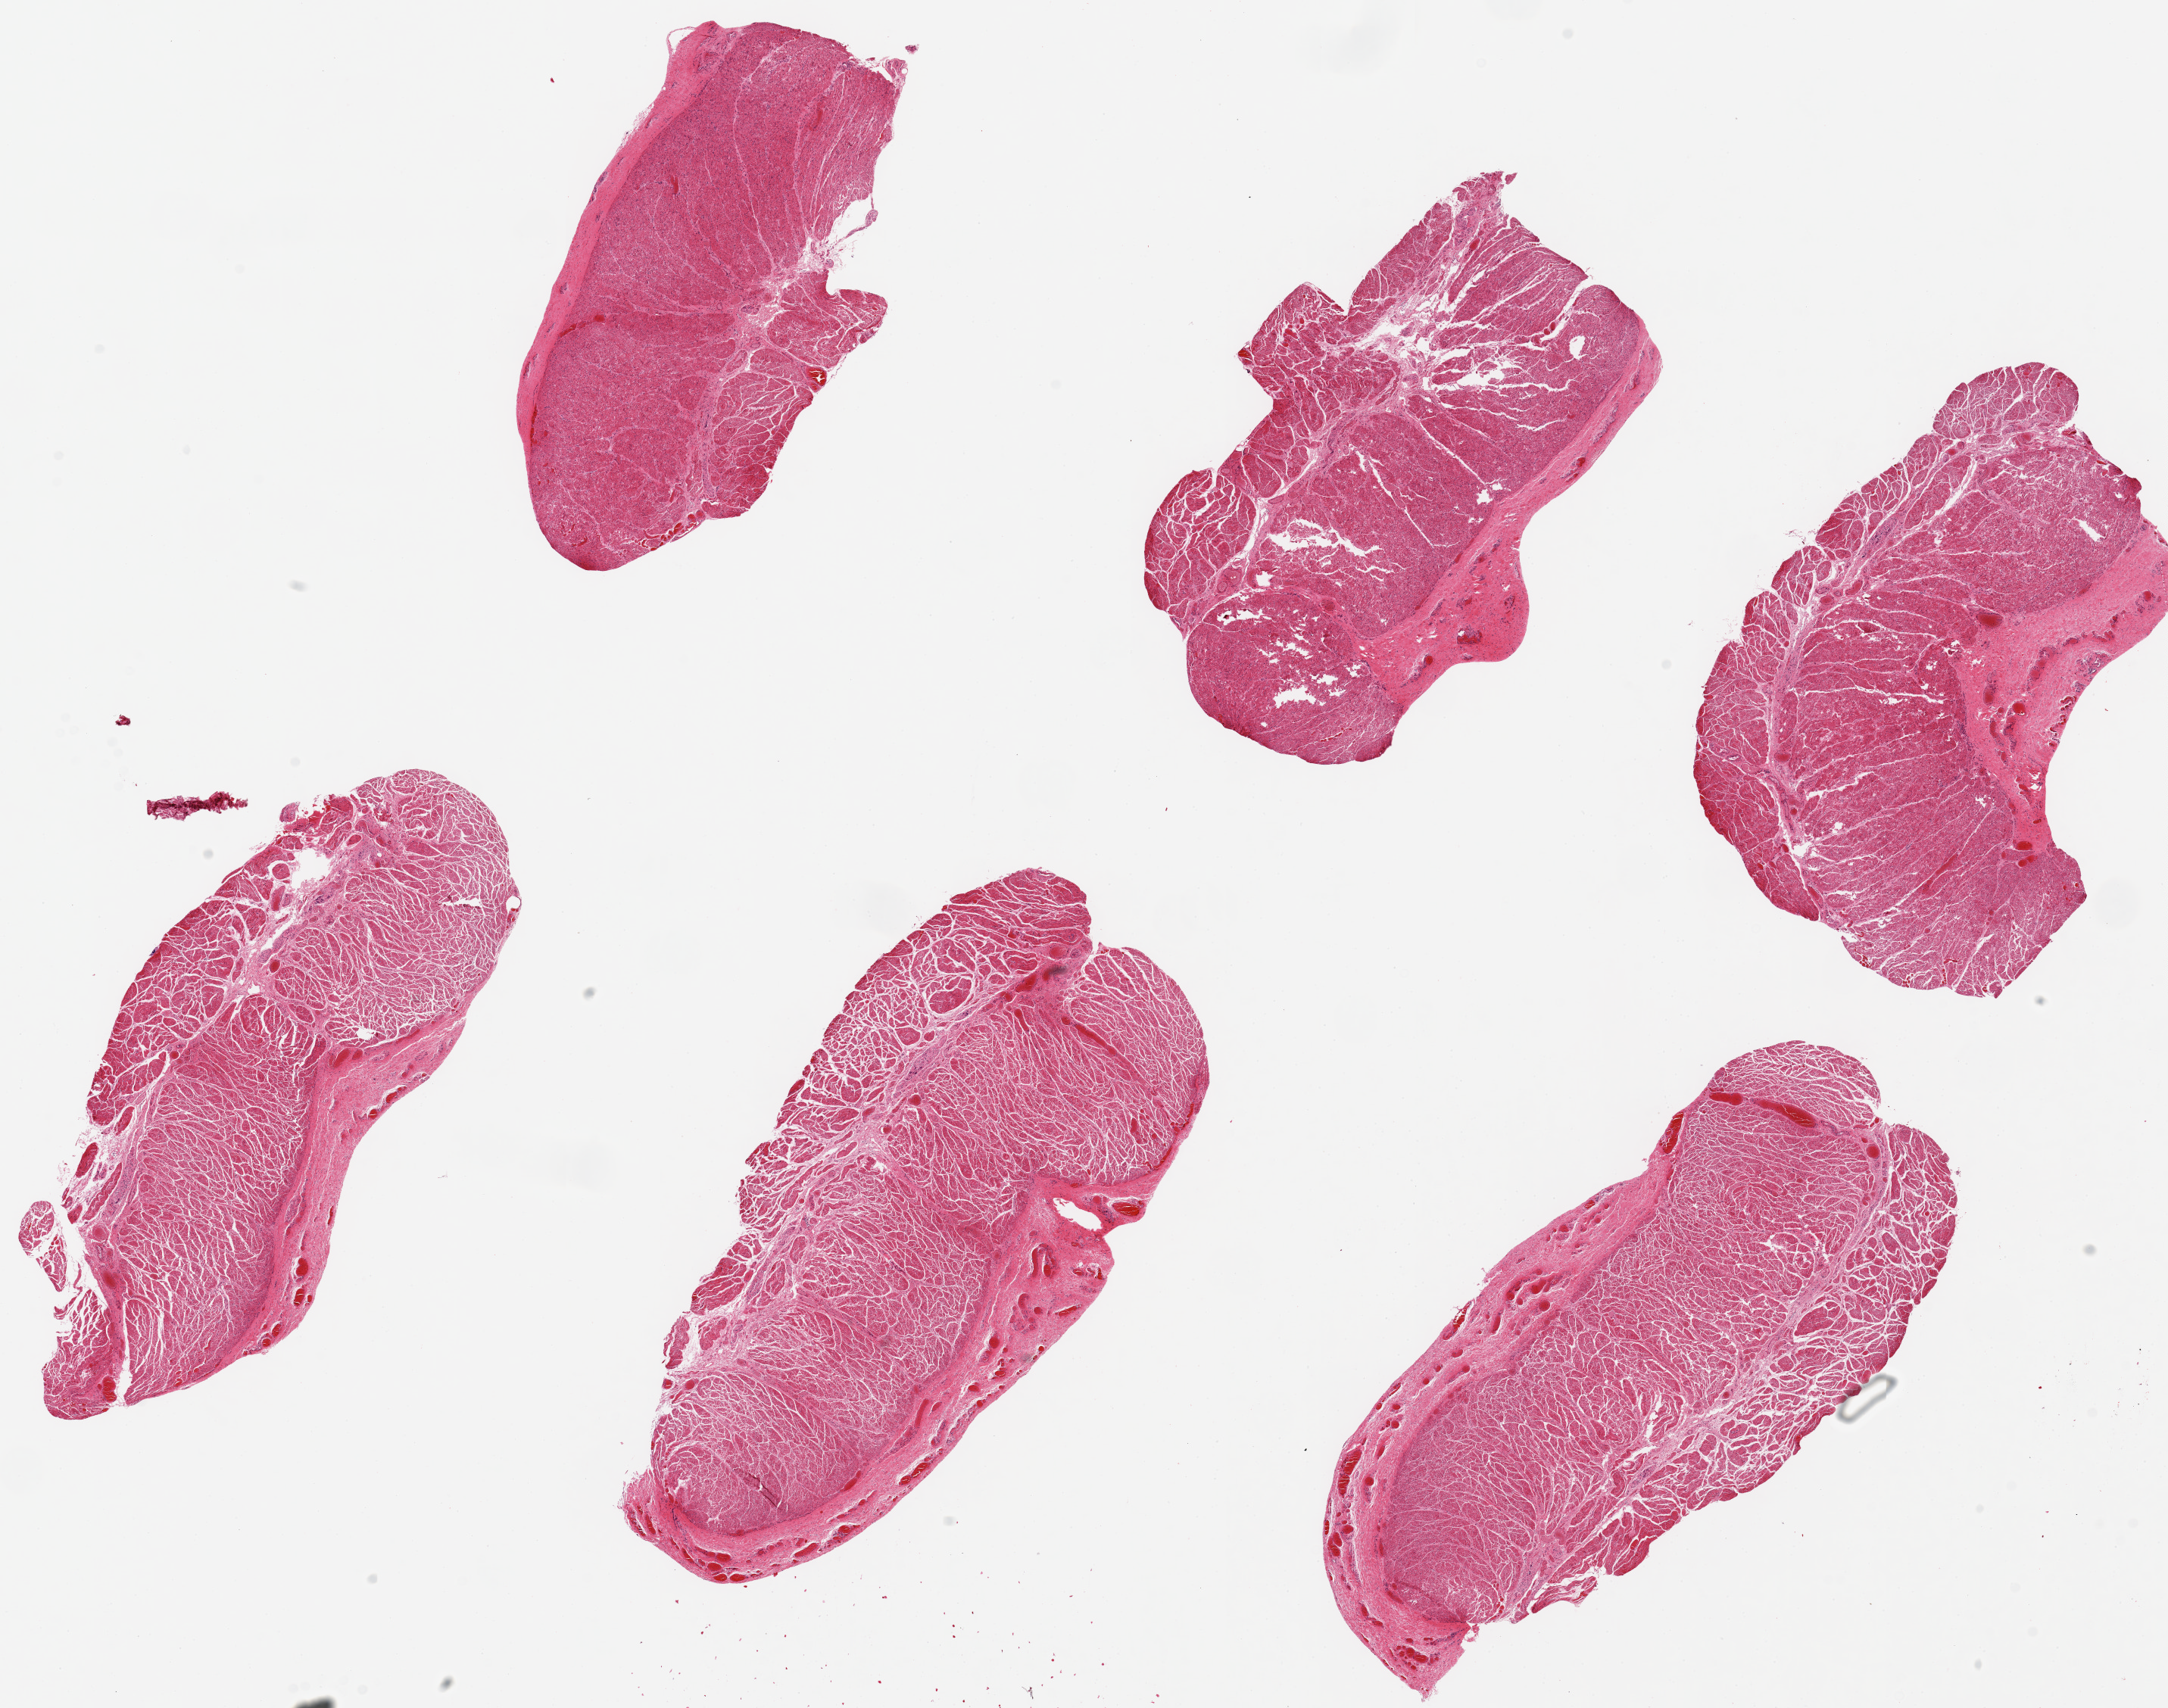
Digitized H&E-stained section — shown as a low-resolution overview of the whole scanned area (about 22.6 x 17.8 mm, slide scanned at 20x), PAXgene-fixed, paraffin-embedded tissue, section of gastroesophageal junction (target tissue), tissue donor sample. Male donor.
• review note (as recorded): 6 pieces, up to 8x4mm; all muscularis, good specimens